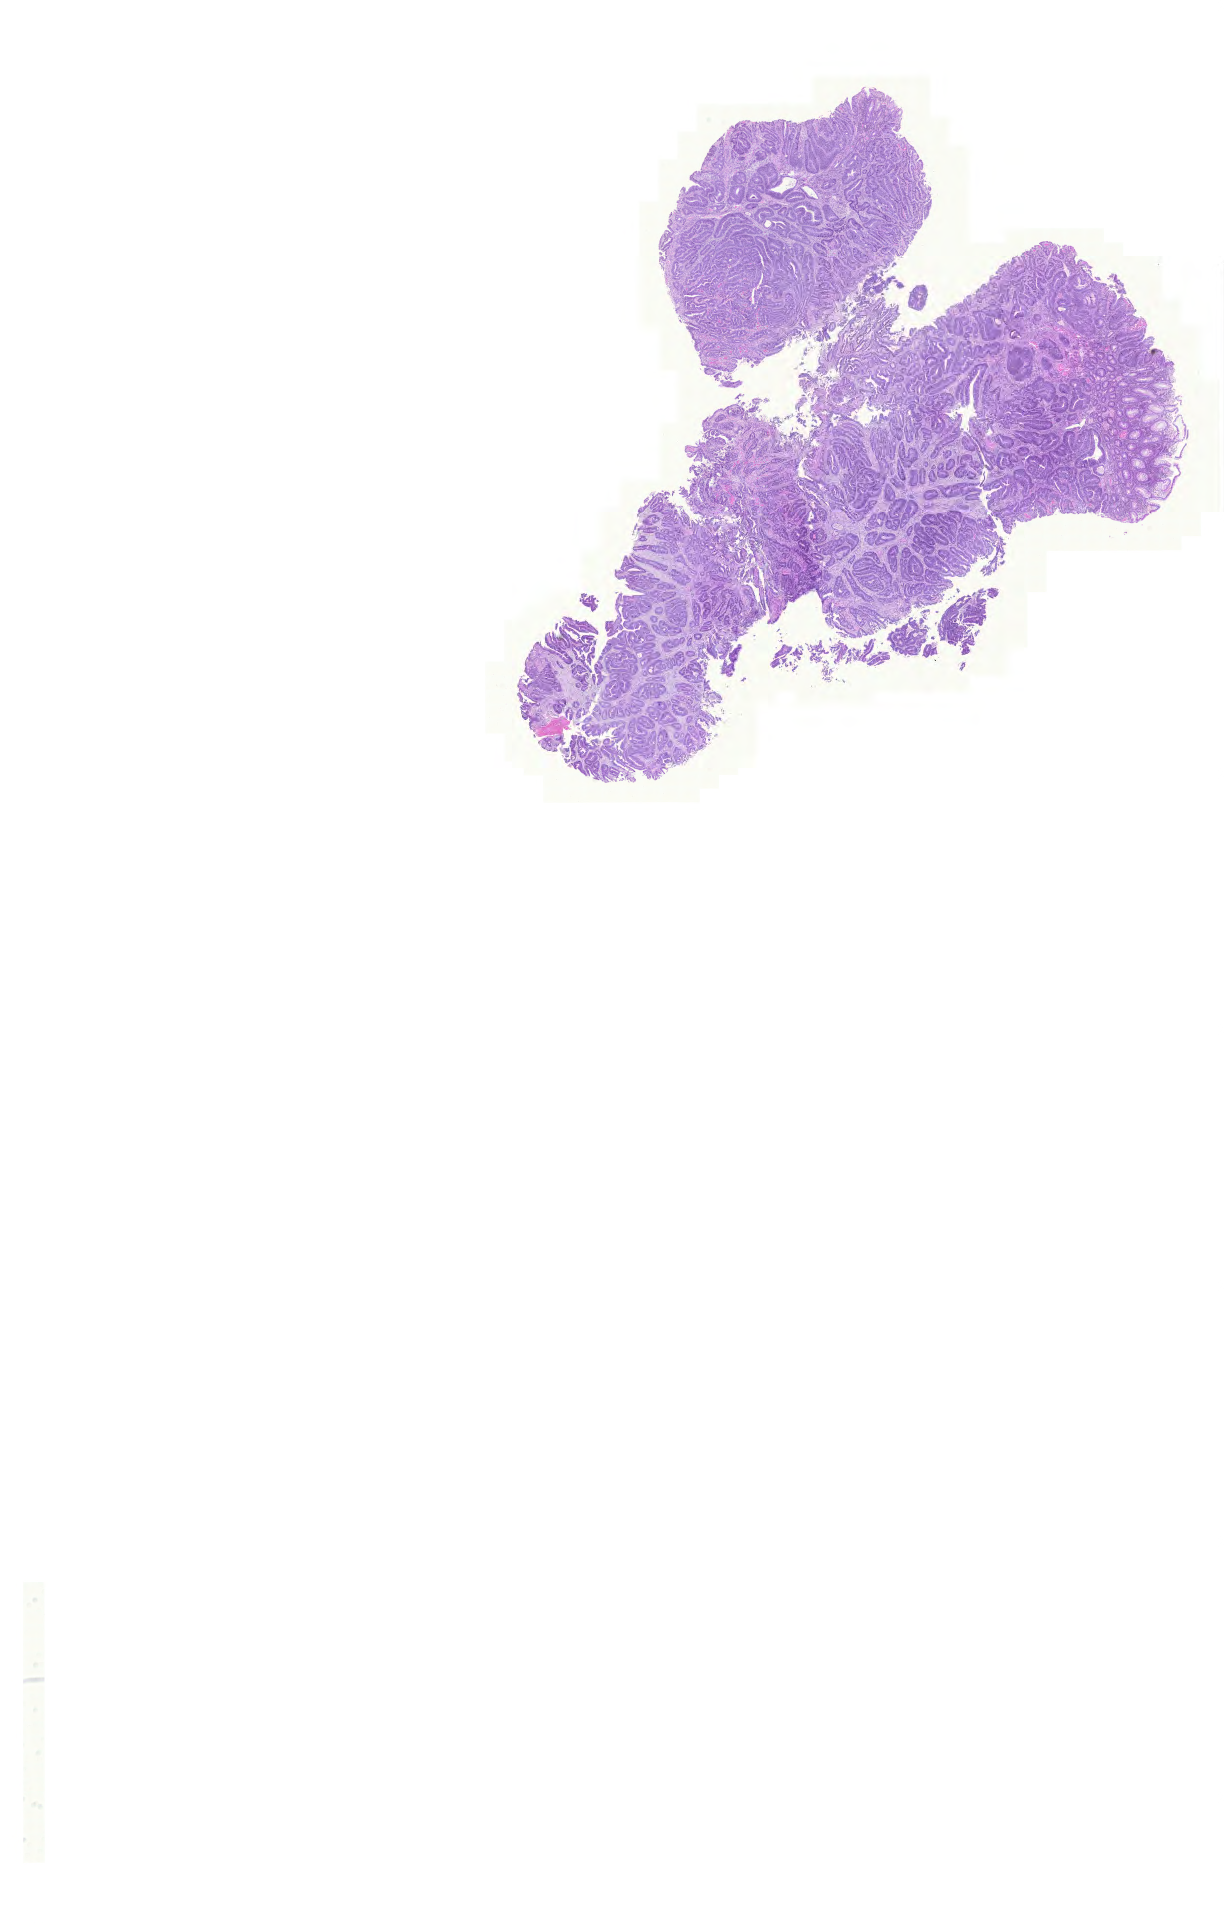
H&E whole-slide image, low-resolution overview of the scanned area, about 18.2 x 28.6 mm. FFPE section. Sample: primary tumour, colon. Male patient; age at initial diagnosis 69 years.
* lymph nodes positive (case pathology): 0 of 24 examined
* AJCC pathologic stage: II (5th edition)
* diagnosis: Adenocarcinoma, NOS